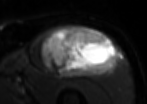
MRI of an extremity soft-tissue mass, one axial slice; position 57 of 85 along the scan axis; T2-weighted fat-saturated; MR volume resampled by the dataset authors to the PET/CT grid (not the native acquisition matrix); 3.27 mm slice thickness; 147 × 104 image matrix, field of view 144 × 102 mm. Male patient. From the clinical record (not read from this slice): histological type: extraskeletal osteosarcoma; grade: high; site of the primary tumour: thigh.
Structures marked on this image (expert contour drawn on MRI and transferred to this co-registered scan by the dataset authors):
- gross tumour volume (mass): bounding box [x1, y1, x2, y2] px = [40, 26, 118, 77]